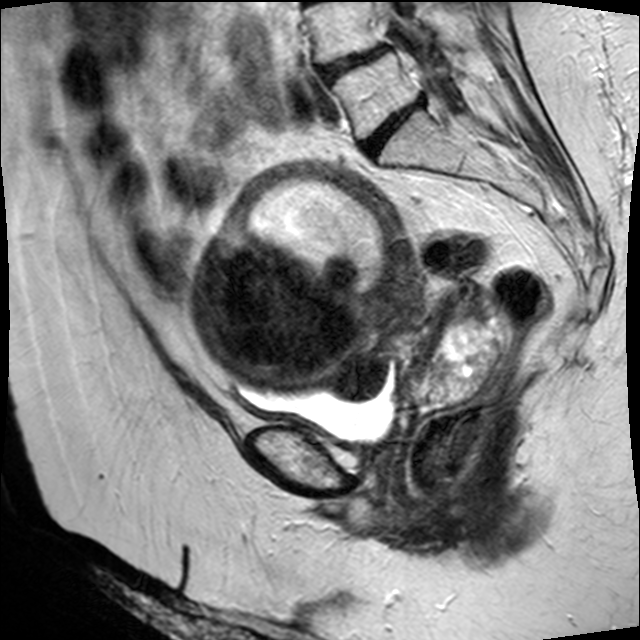
Pelvic MRI for cervical cancer, one sagittal slice. Position 25 of 45 along the scan axis. T2-weighted. 1.5 T. TE 89 ms, TR 4610 ms. 4 mm slice thickness. 640 × 640 image matrix, field of view 260 × 260 mm. Patient: female, 50 years.
Structures marked on this image (outlined manually by an expert reader):
- uterus and cervix: bounding box [x1, y1, x2, y2] px = [201, 162, 499, 408]